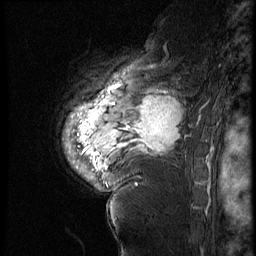
Breast MRI (dynamic contrast-enhanced), one sagittal slice; slice 48 of 60 in the series (ordered by position); 4 images stored at this slice position (order not interpretable as contrast timing); 1.5 T; TE 4.2 ms, TR 9 ms; 256 × 256 image matrix, field of view 180 × 180 mm. Female patient, age 56 years. From the clinical record (not read from this slice): setting: breast cancer imaged before/during neoadjuvant chemotherapy; receptor status: HER2-positive.
Outlined on this slice (semi-automatic segmentation, software-assisted and operator-edited):
- analysis volume of interest (the breast-tissue region the enhancement analysis was run in; not a lesion): bounding box (x1, y1, x2, y2) in pixels: (82, 83, 199, 177)
- tumour enhancement mask (voxels above the 140 % enhancement threshold inside the analysis volume of interest): (95, 97, 182, 163)